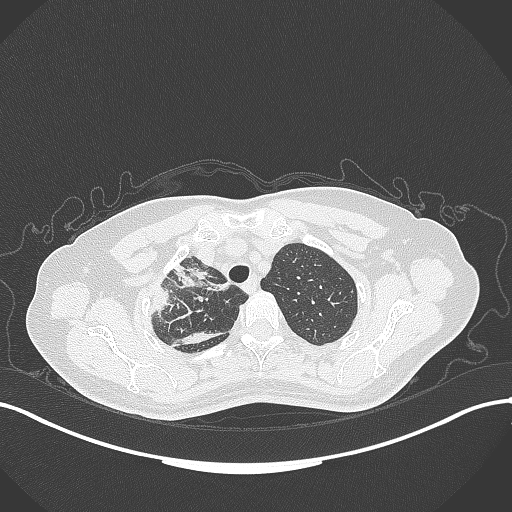
Chest CT, one axial slice. Slice 267 of 309 in the series (ordered by position). 120 kVp. Lung window (W 1500 / L -600 HU). 512 × 512 image matrix. Patient: female, 60 years. Case-level facts recorded for this patient, not image findings: clinical TNM (as recorded): T3 N1 M1.
Outlined on this slice (bounding box drawn by a radiologist):
- lung tumour (recorded histology: adenocarcinoma): bounding box [x1, y1, x2, y2] px = [165, 254, 233, 300]